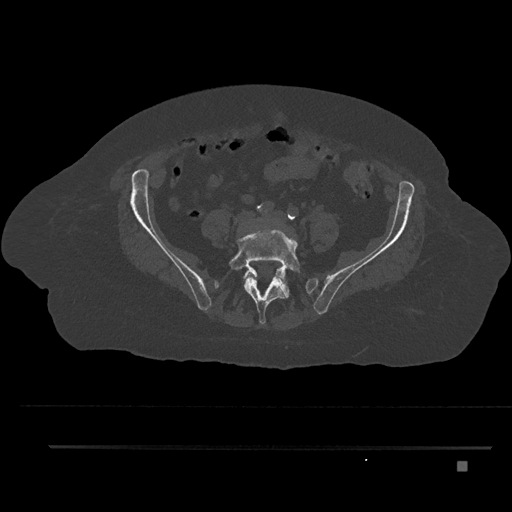
CT including the spine, one axial slice. Slice 40 of 797 in the series (ordered by position). 120 kVp. Bone window (W 1800 / L 400 HU). 512 × 512 image matrix, field of view 437 × 437 mm. Patient: female, 76 years. From the clinical record (not read from this slice): primary cancer: lung; vertebrae with lytic lesions (as recorded): T11, L3.
Outlined on this slice (semi-automatically segmented with operator editing):
- L4 vertebra: bounding box [x1, y1, x2, y2] px = [246, 272, 287, 284]
- L5 vertebra: [228, 220, 300, 325]